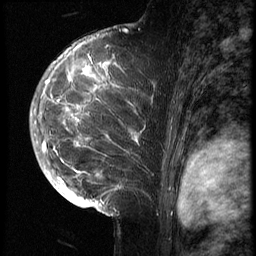
Breast MRI (dynamic contrast-enhanced), one sagittal slice; position 42 of 70 along the scan axis; 3 images stored at this slice position (order not interpretable as contrast timing); 1.5 T; TE 4.2 ms, TR 9 ms; 2.5 mm slice thickness; 256 × 256 image matrix. Female patient, age 28 years. Case-level facts recorded for this patient, not image findings: setting: breast cancer imaged before/during neoadjuvant chemotherapy.
Structures marked on this image (semi-automatically segmented with operator editing):
- analysis volume of interest (the breast-tissue region the enhancement analysis was run in; not a lesion): bounding box (x1, y1, x2, y2) in pixels: (43, 42, 160, 215)
- tumour enhancement mask (voxels above the 140 % enhancement threshold inside the analysis volume of interest): (43, 46, 139, 206)